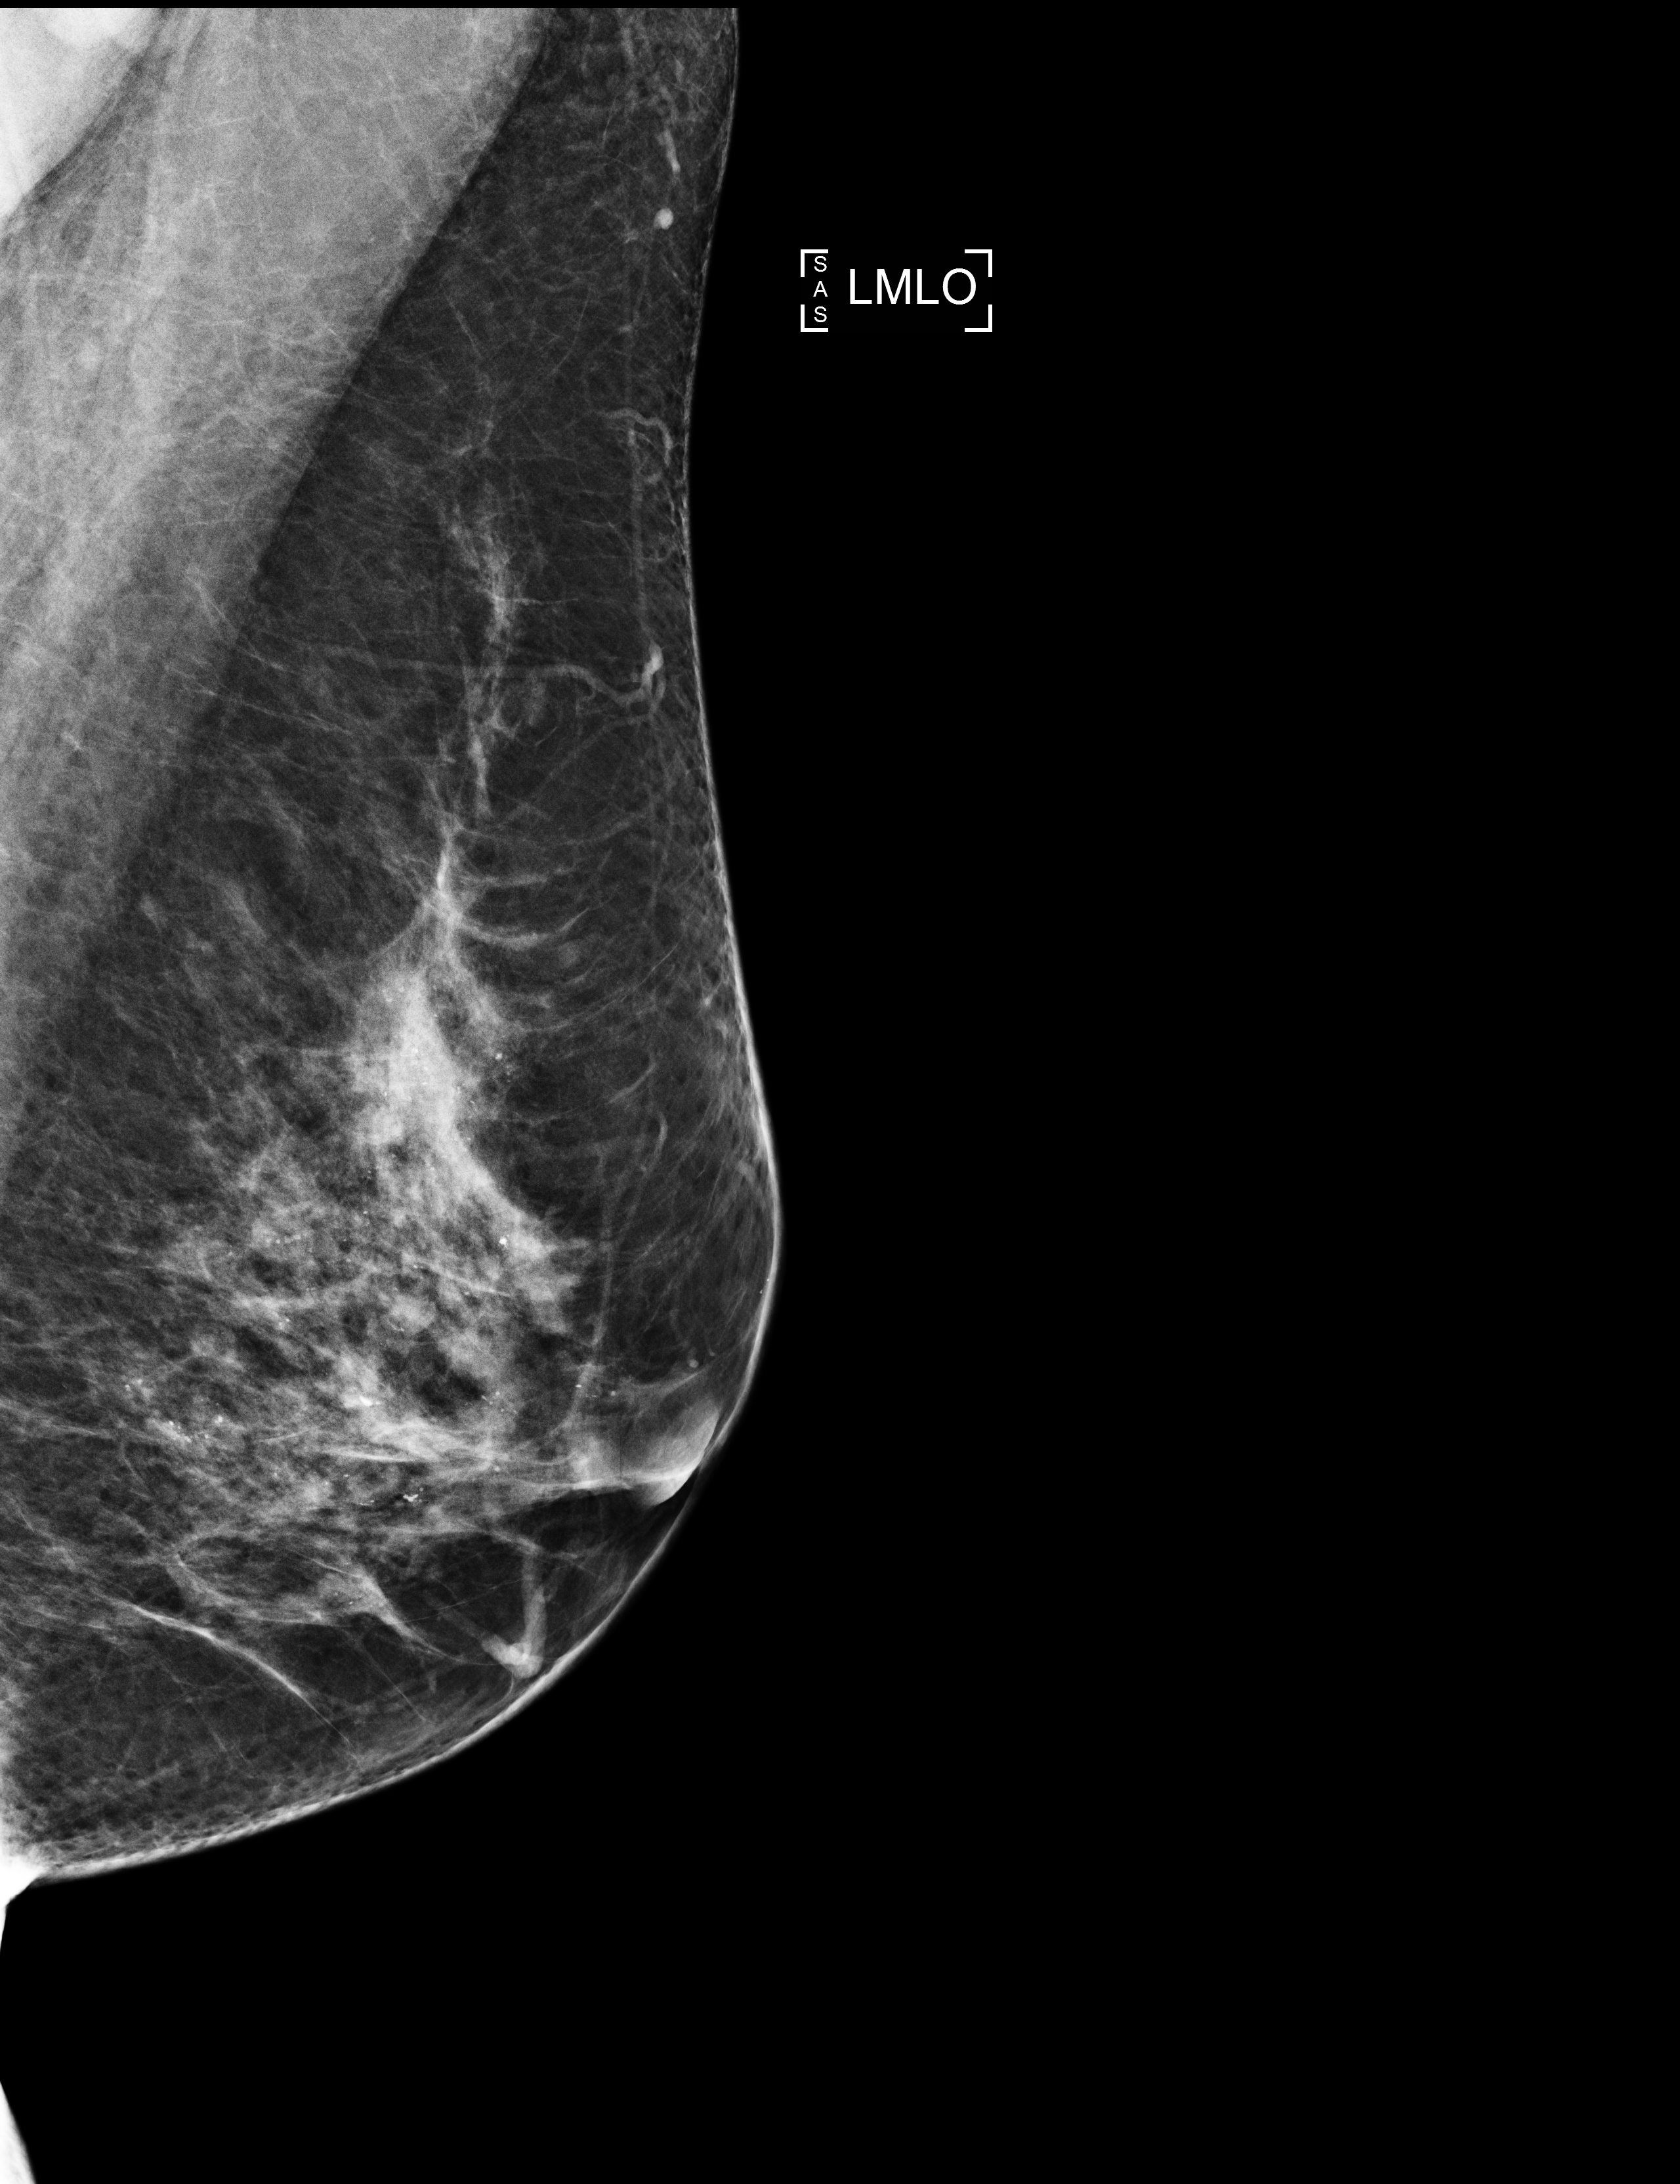
Annual screening mammography examination, compressed breast thickness 63 mm, system: Selenia Dimensions. Patient aged 51 years (female).
Image type: full-field digital mammogram. Breast: left. Projection: MLO view.